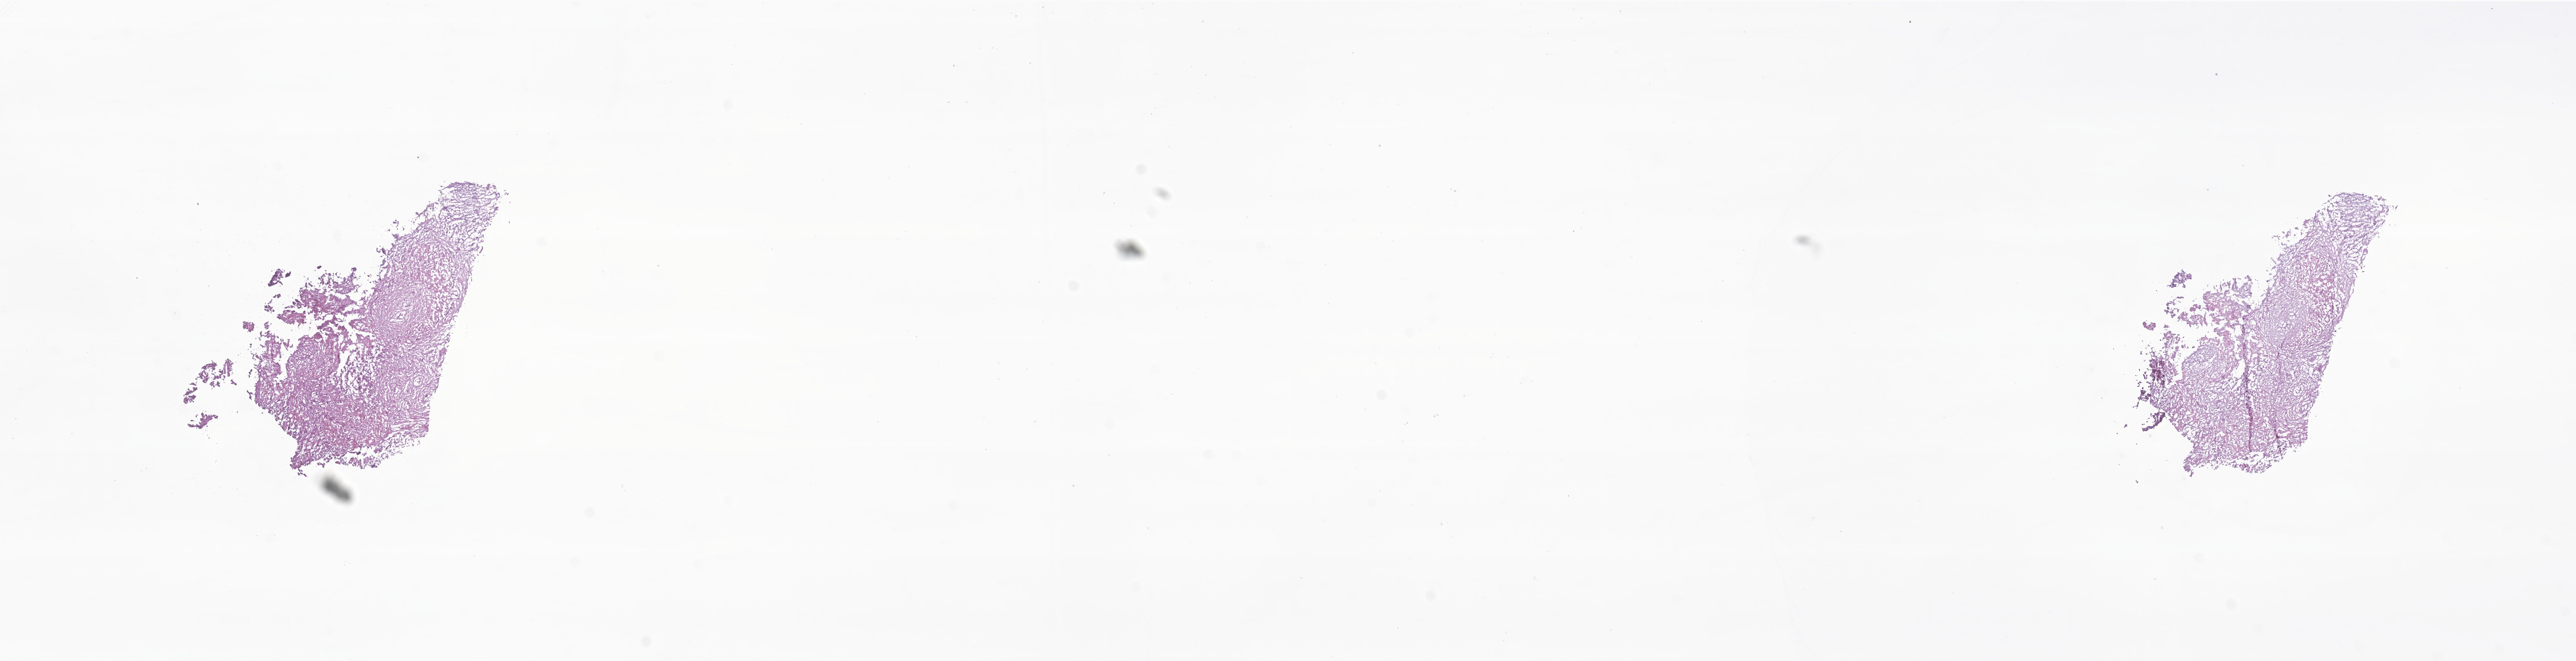
H&E whole-slide image of tumor tissue from the brain, shown as a low-resolution overview of the whole scanned area (about 25.9 x 6.7 mm). Frozen section. Patient female; age 214 days.
Diagnosis (ICD-O-3 morphology term): Ependymoma, NOS.